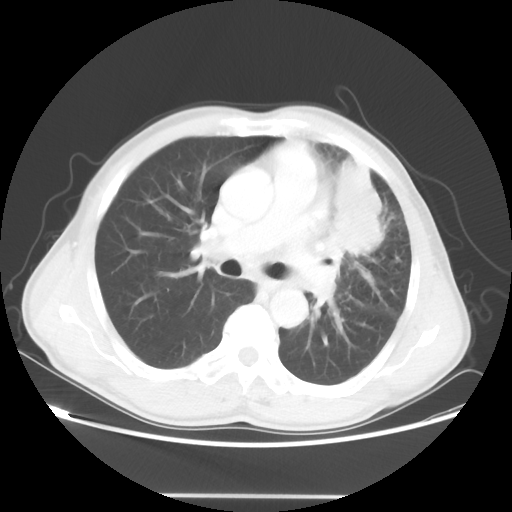
Chest CT, one axial slice; slice 31 of 55 in the series (ordered by position); 100 kVp; lung window (W 1500 / L -600 HU); 5 mm slice thickness; 512 × 512 image matrix, field of view 398 × 398 mm. Patient: male, 60 years. Case-level facts recorded for this patient, not image findings: clinical TNM (as recorded): T3 N3 M0.
Outlined on this slice (bounding box drawn by a radiologist):
- lung tumour (recorded histology: adenocarcinoma): box from (x=332, y=157) to (x=389, y=261) px